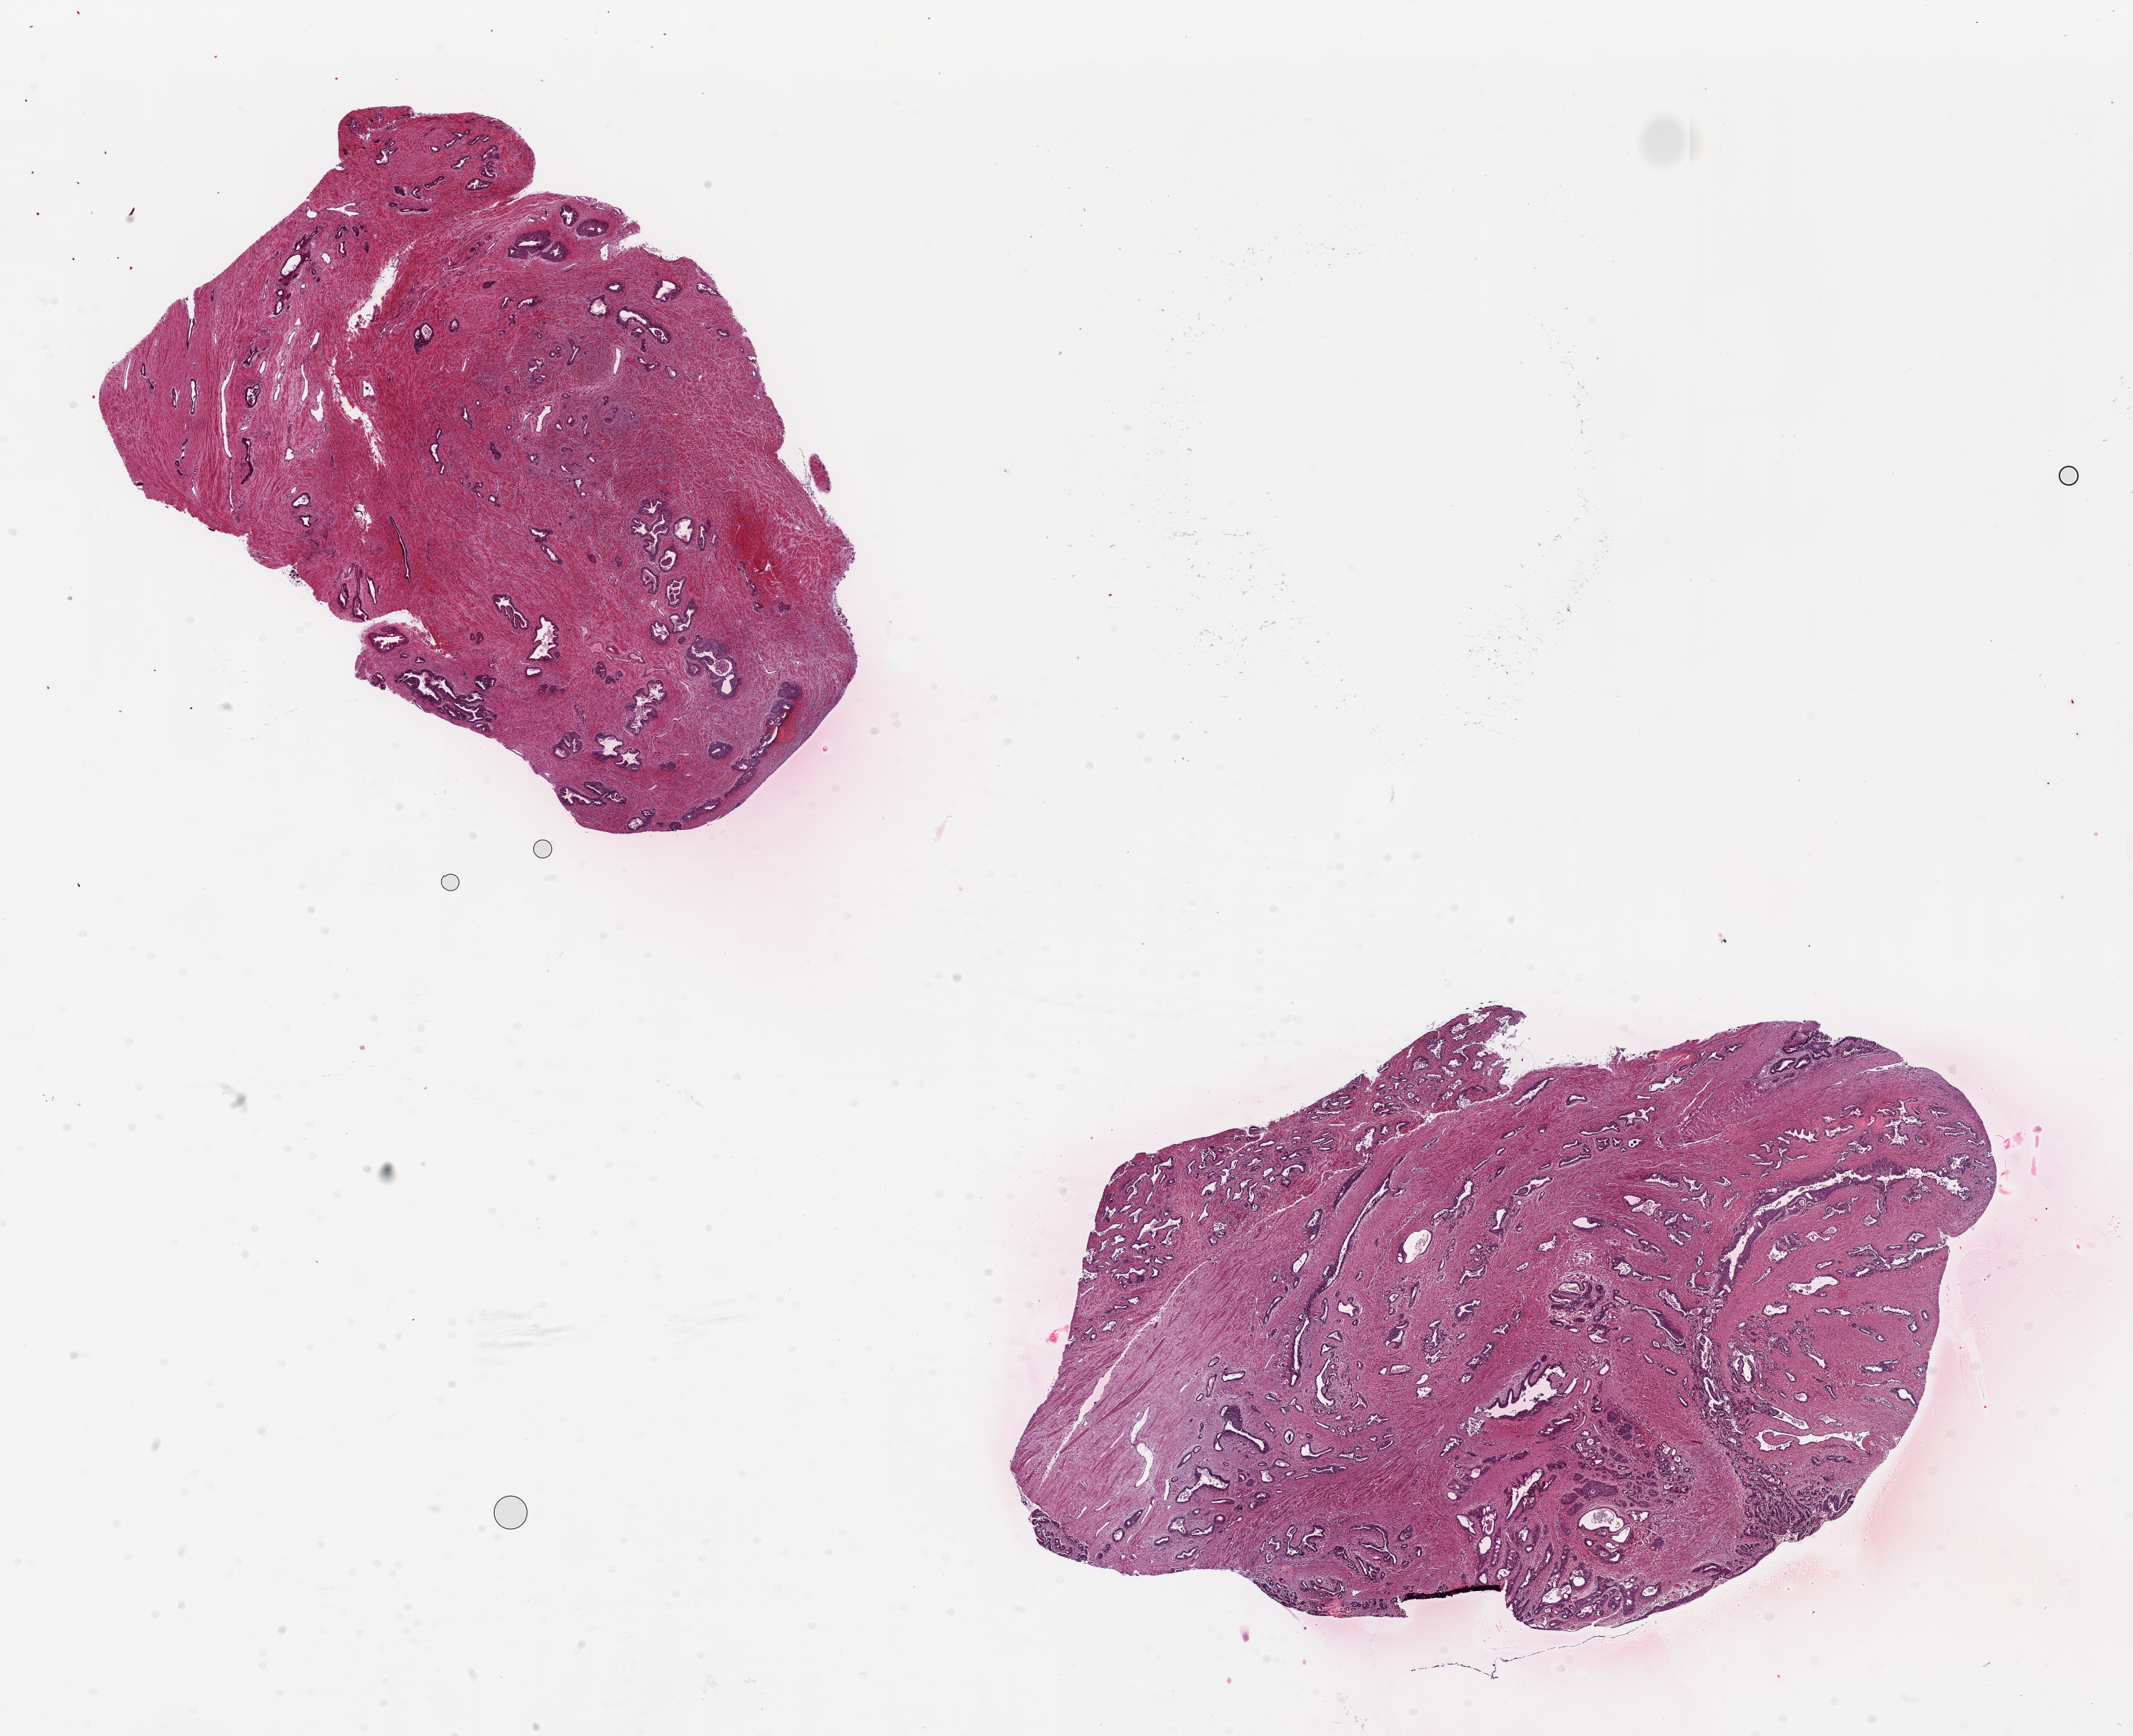
Haematoxylin and eosin whole-slide image, whole scanned area (about 23.6 x 19.2 mm) shown as a low-resolution overview; PAXgene-fixed paraffin-embedded (PFPE) section; target tissue: prostate; tissue donor sample. Male donor.
Pathologist's review note for this sample: 2 pieces ~9x6mm. Glands reasonably well preserved, hyperplastic foci.